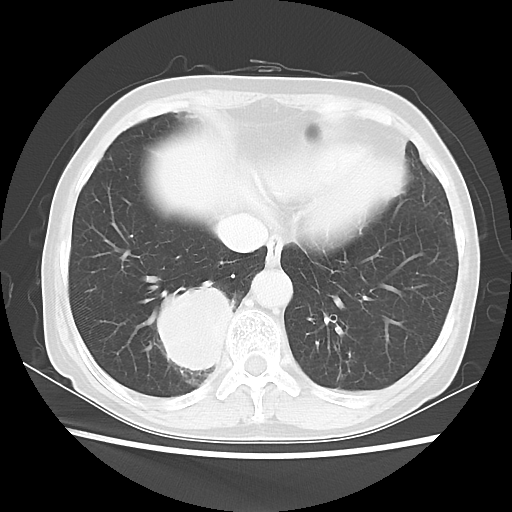
Chest CT, one axial slice; slice 15 of 56 in the series (ordered by position); reconstruction kernel LUNG; 120 kVp; lung window (W 1500 / L -600 HU); 5 mm slice thickness; 512 × 512 image matrix. Female patient, age 66 years. From the clinical record (not read from this slice): clinical TNM (as recorded): T2 N3 M0; histopathological grade: G3.
Structures marked on this image (bounding box drawn by a radiologist):
- lung tumour (recorded histology: small cell carcinoma): bounding box <144,268,246,375> (left, top, right, bottom; pixels)